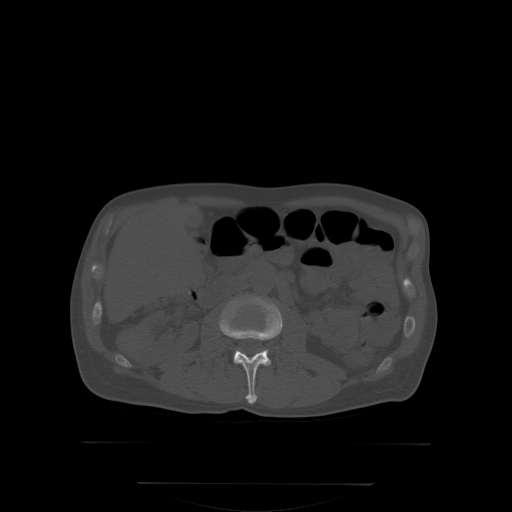
CT including the spine, one axial slice. Slice 134 of 350 in the series (ordered by position). Bone window (W 1800 / L 400 HU). 2.5 mm slice thickness. 512 × 512 image matrix. Male patient, age 58 years. Case-level facts recorded for this patient, not image findings: primary cancer: prostate; vertebrae with lytic lesions (as recorded): L1.
Annotated regions visible in this slice (semi-automatically segmented with operator editing):
- L2 vertebra: bounding box <221,296,282,402> (left, top, right, bottom; pixels)